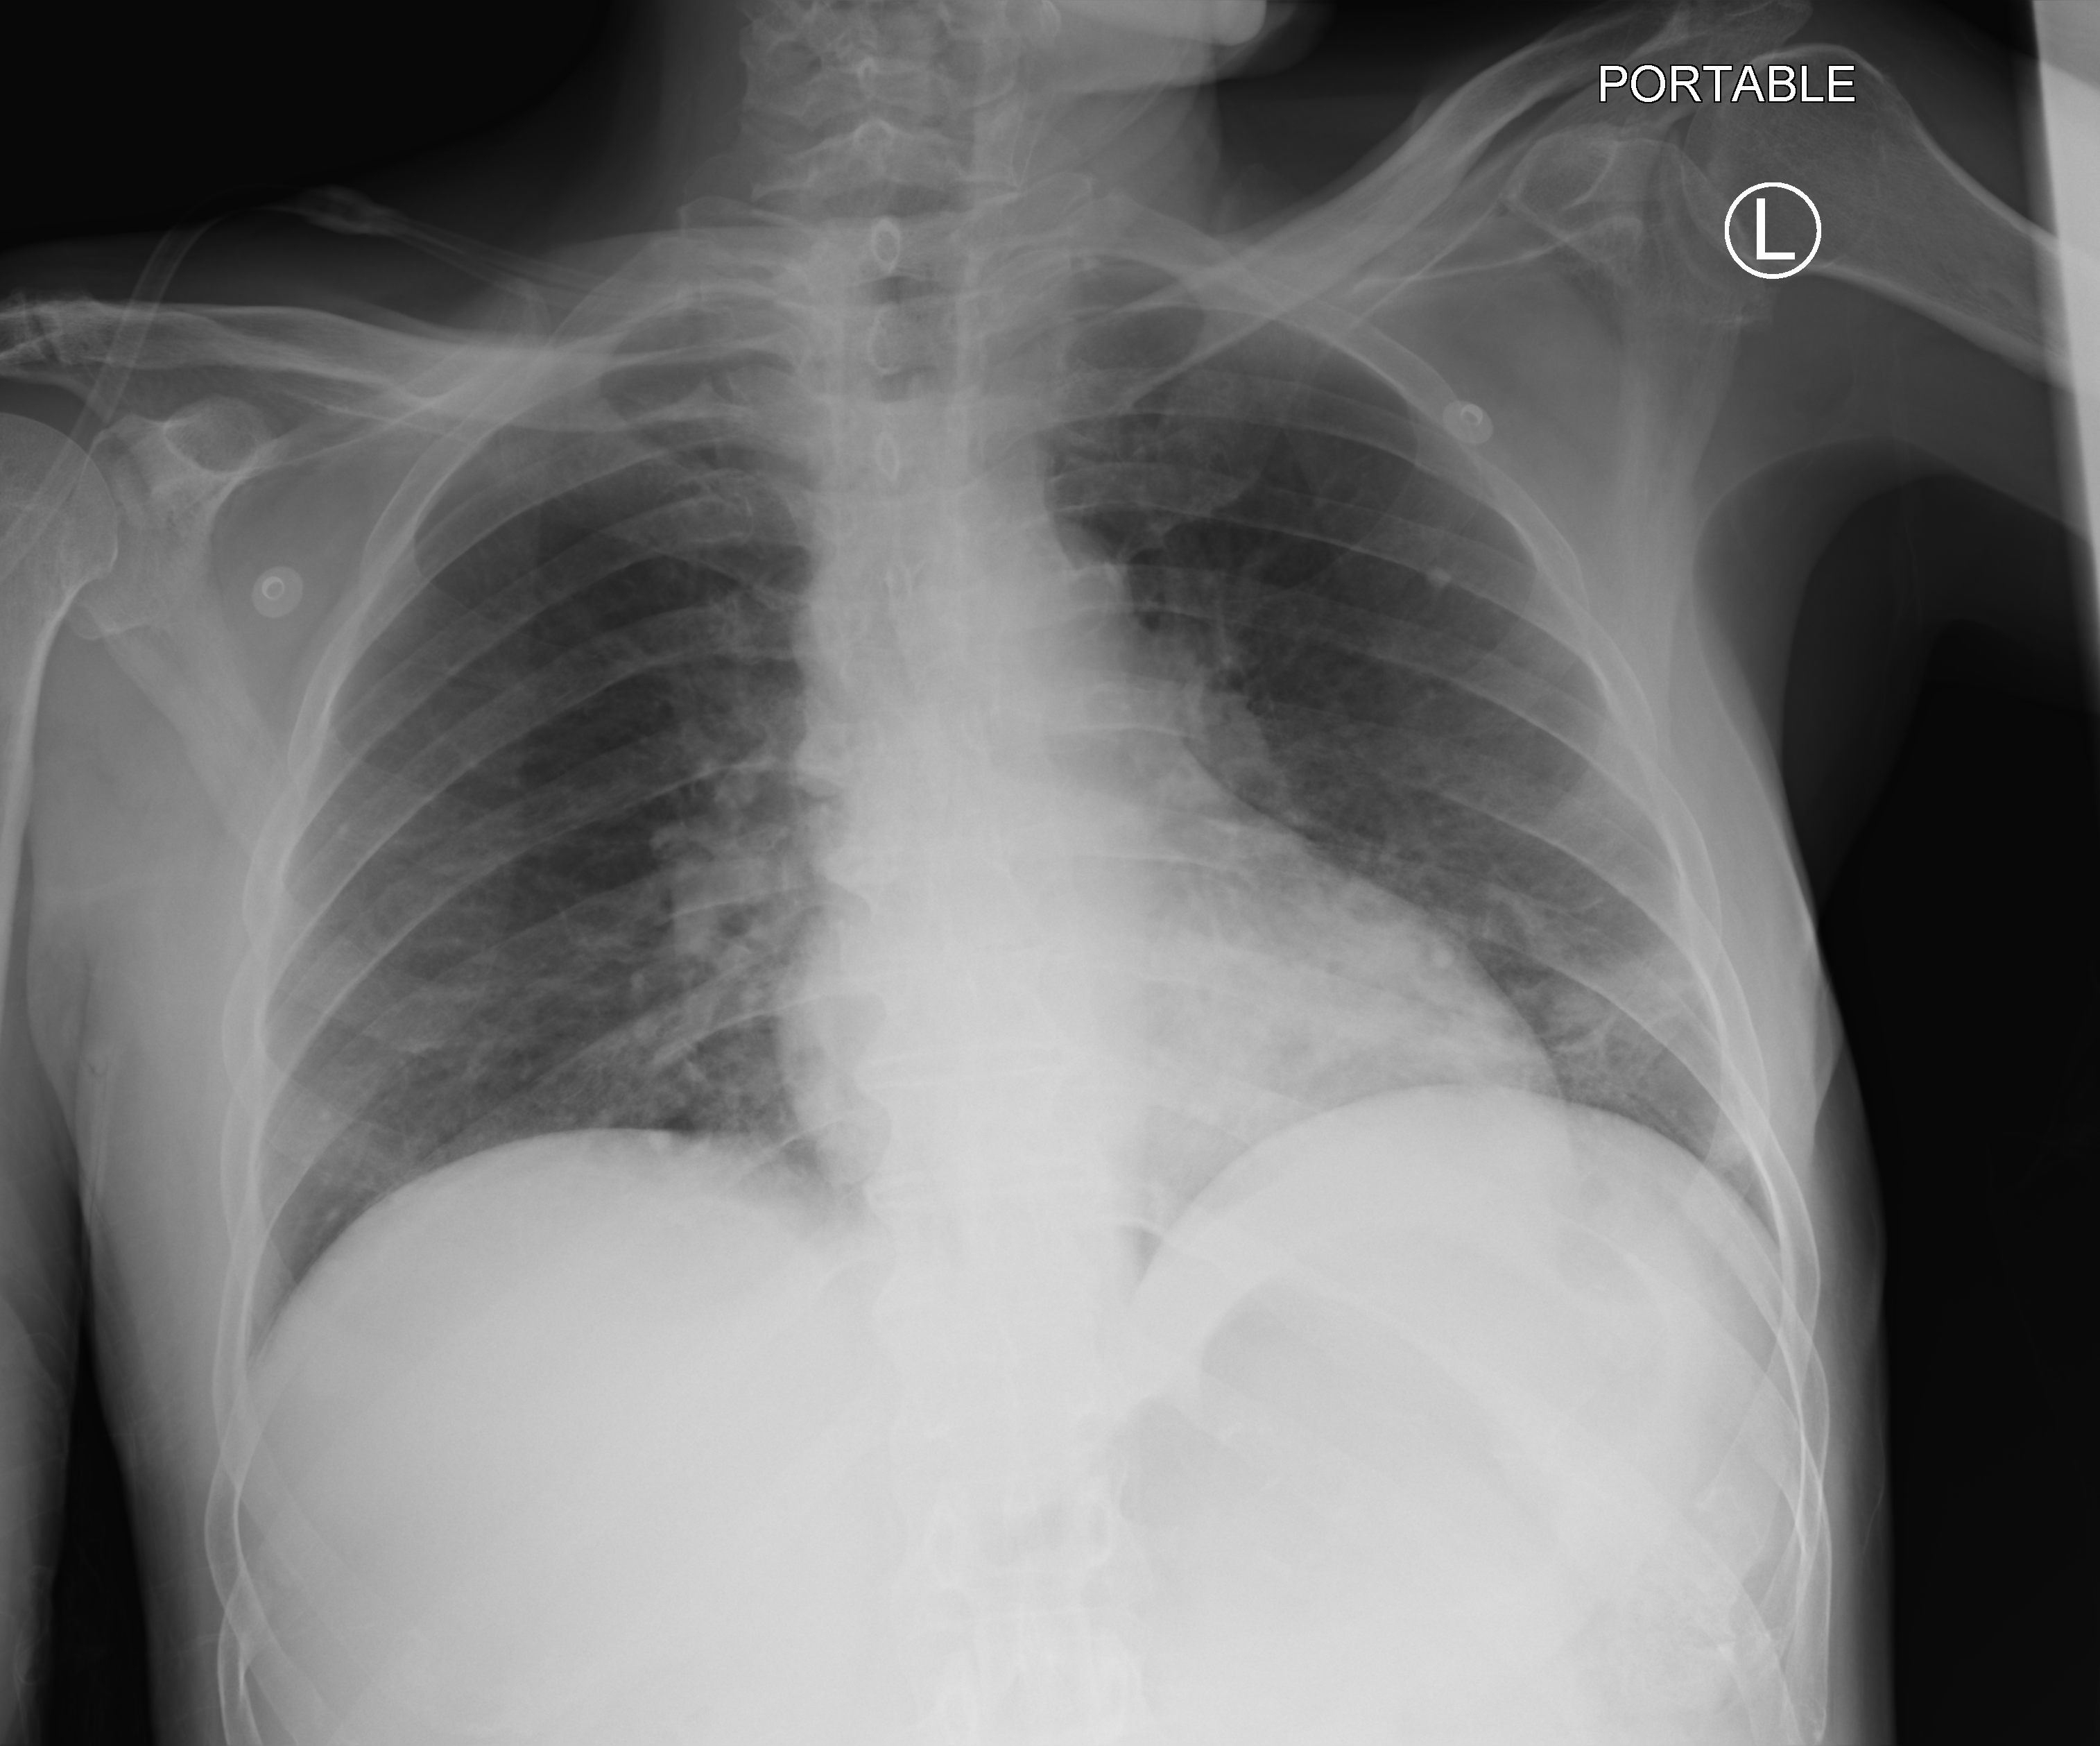
Chest X-ray (portable), anteroposterior (AP) projection. Patient hospitalised with COVID-19; male, aged 60–74 years.
From the hospital-stay record, not from the radiograph (when in the stay this image was taken is not recorded):
- admitted to intensive care during this hospital stay: no